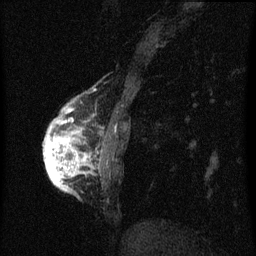
Breast MRI (dynamic contrast-enhanced), one sagittal slice; position 15 of 60 along the scan axis; dynamic contrast-enhanced series, image 2 of 3 at this slice position (ordered by acquisition); 1.5 T; TE 4.2 ms, TR 8 ms; 256 × 256 image matrix. Patient: female, 56 years.
Annotated regions visible in this slice (semi-automatically segmented with operator editing):
- analysis volume of interest (the breast-tissue region the enhancement analysis was run in; not a lesion): bounding box <44,110,95,191> (left, top, right, bottom; pixels)
- tumour enhancement mask (voxels above the 70 % enhancement threshold inside the analysis volume of interest): <44,120,87,191>